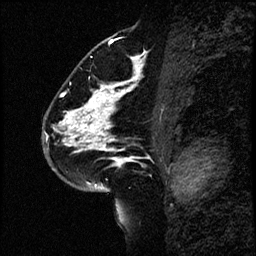
Breast MRI (dynamic contrast-enhanced), one sagittal slice; dynamic contrast-enhanced study with each time point stored as its own series, time point 2 of 4 at this slice position (early post-contrast, ordered by acquisition time); 1.5 T; TE 4.2 ms, TR 17.6 ms; 256 × 256 image matrix, field of view 200 × 200 mm. Patient: female, 43 years. Case-level facts recorded for this patient, not image findings: setting: breast cancer imaged before/during neoadjuvant chemotherapy.
Outlined on this slice (semi-automatic segmentation, software-assisted and operator-edited):
- analysis volume of interest (the breast-tissue region the enhancement analysis was run in; not a lesion): bounding box [x1, y1, x2, y2] px = [45, 56, 168, 191]
- tumour enhancement mask (voxels above the 100 % enhancement threshold inside the analysis volume of interest): [46, 57, 139, 185]